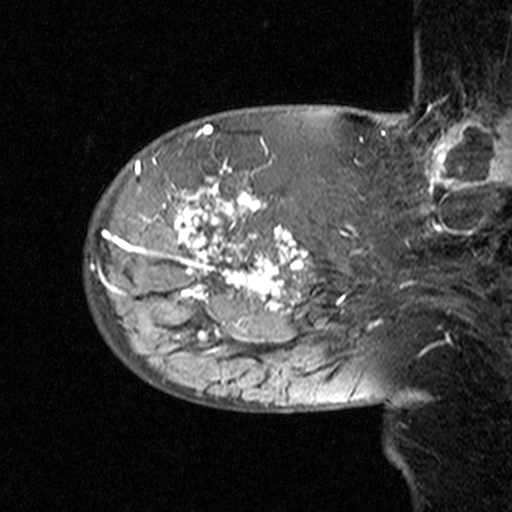
Breast MRI (dynamic contrast-enhanced), one sagittal slice. Position 11 of 44 along the scan axis. Dynamic contrast-enhanced study with each time point stored as its own series, time point 2 of 3 at this slice position (early post-contrast, ordered by acquisition time). 1.5 T. TE 4.5 ms, TR 11 ms. 3 mm slice thickness. 512 × 512 image matrix, field of view 200 × 200 mm. Female patient, age 53 years. From the clinical record (not read from this slice): setting: breast cancer imaged before/during neoadjuvant chemotherapy; receptor status: HR-positive, HER2-negative.
Outlined on this slice (semi-automatically segmented with operator editing):
- analysis volume of interest (the breast-tissue region the enhancement analysis was run in; not a lesion): bounding box <83,140,311,353> (left, top, right, bottom; pixels)
- tumour enhancement mask (voxels above the 90 % enhancement threshold inside the analysis volume of interest): <97,177,309,341>